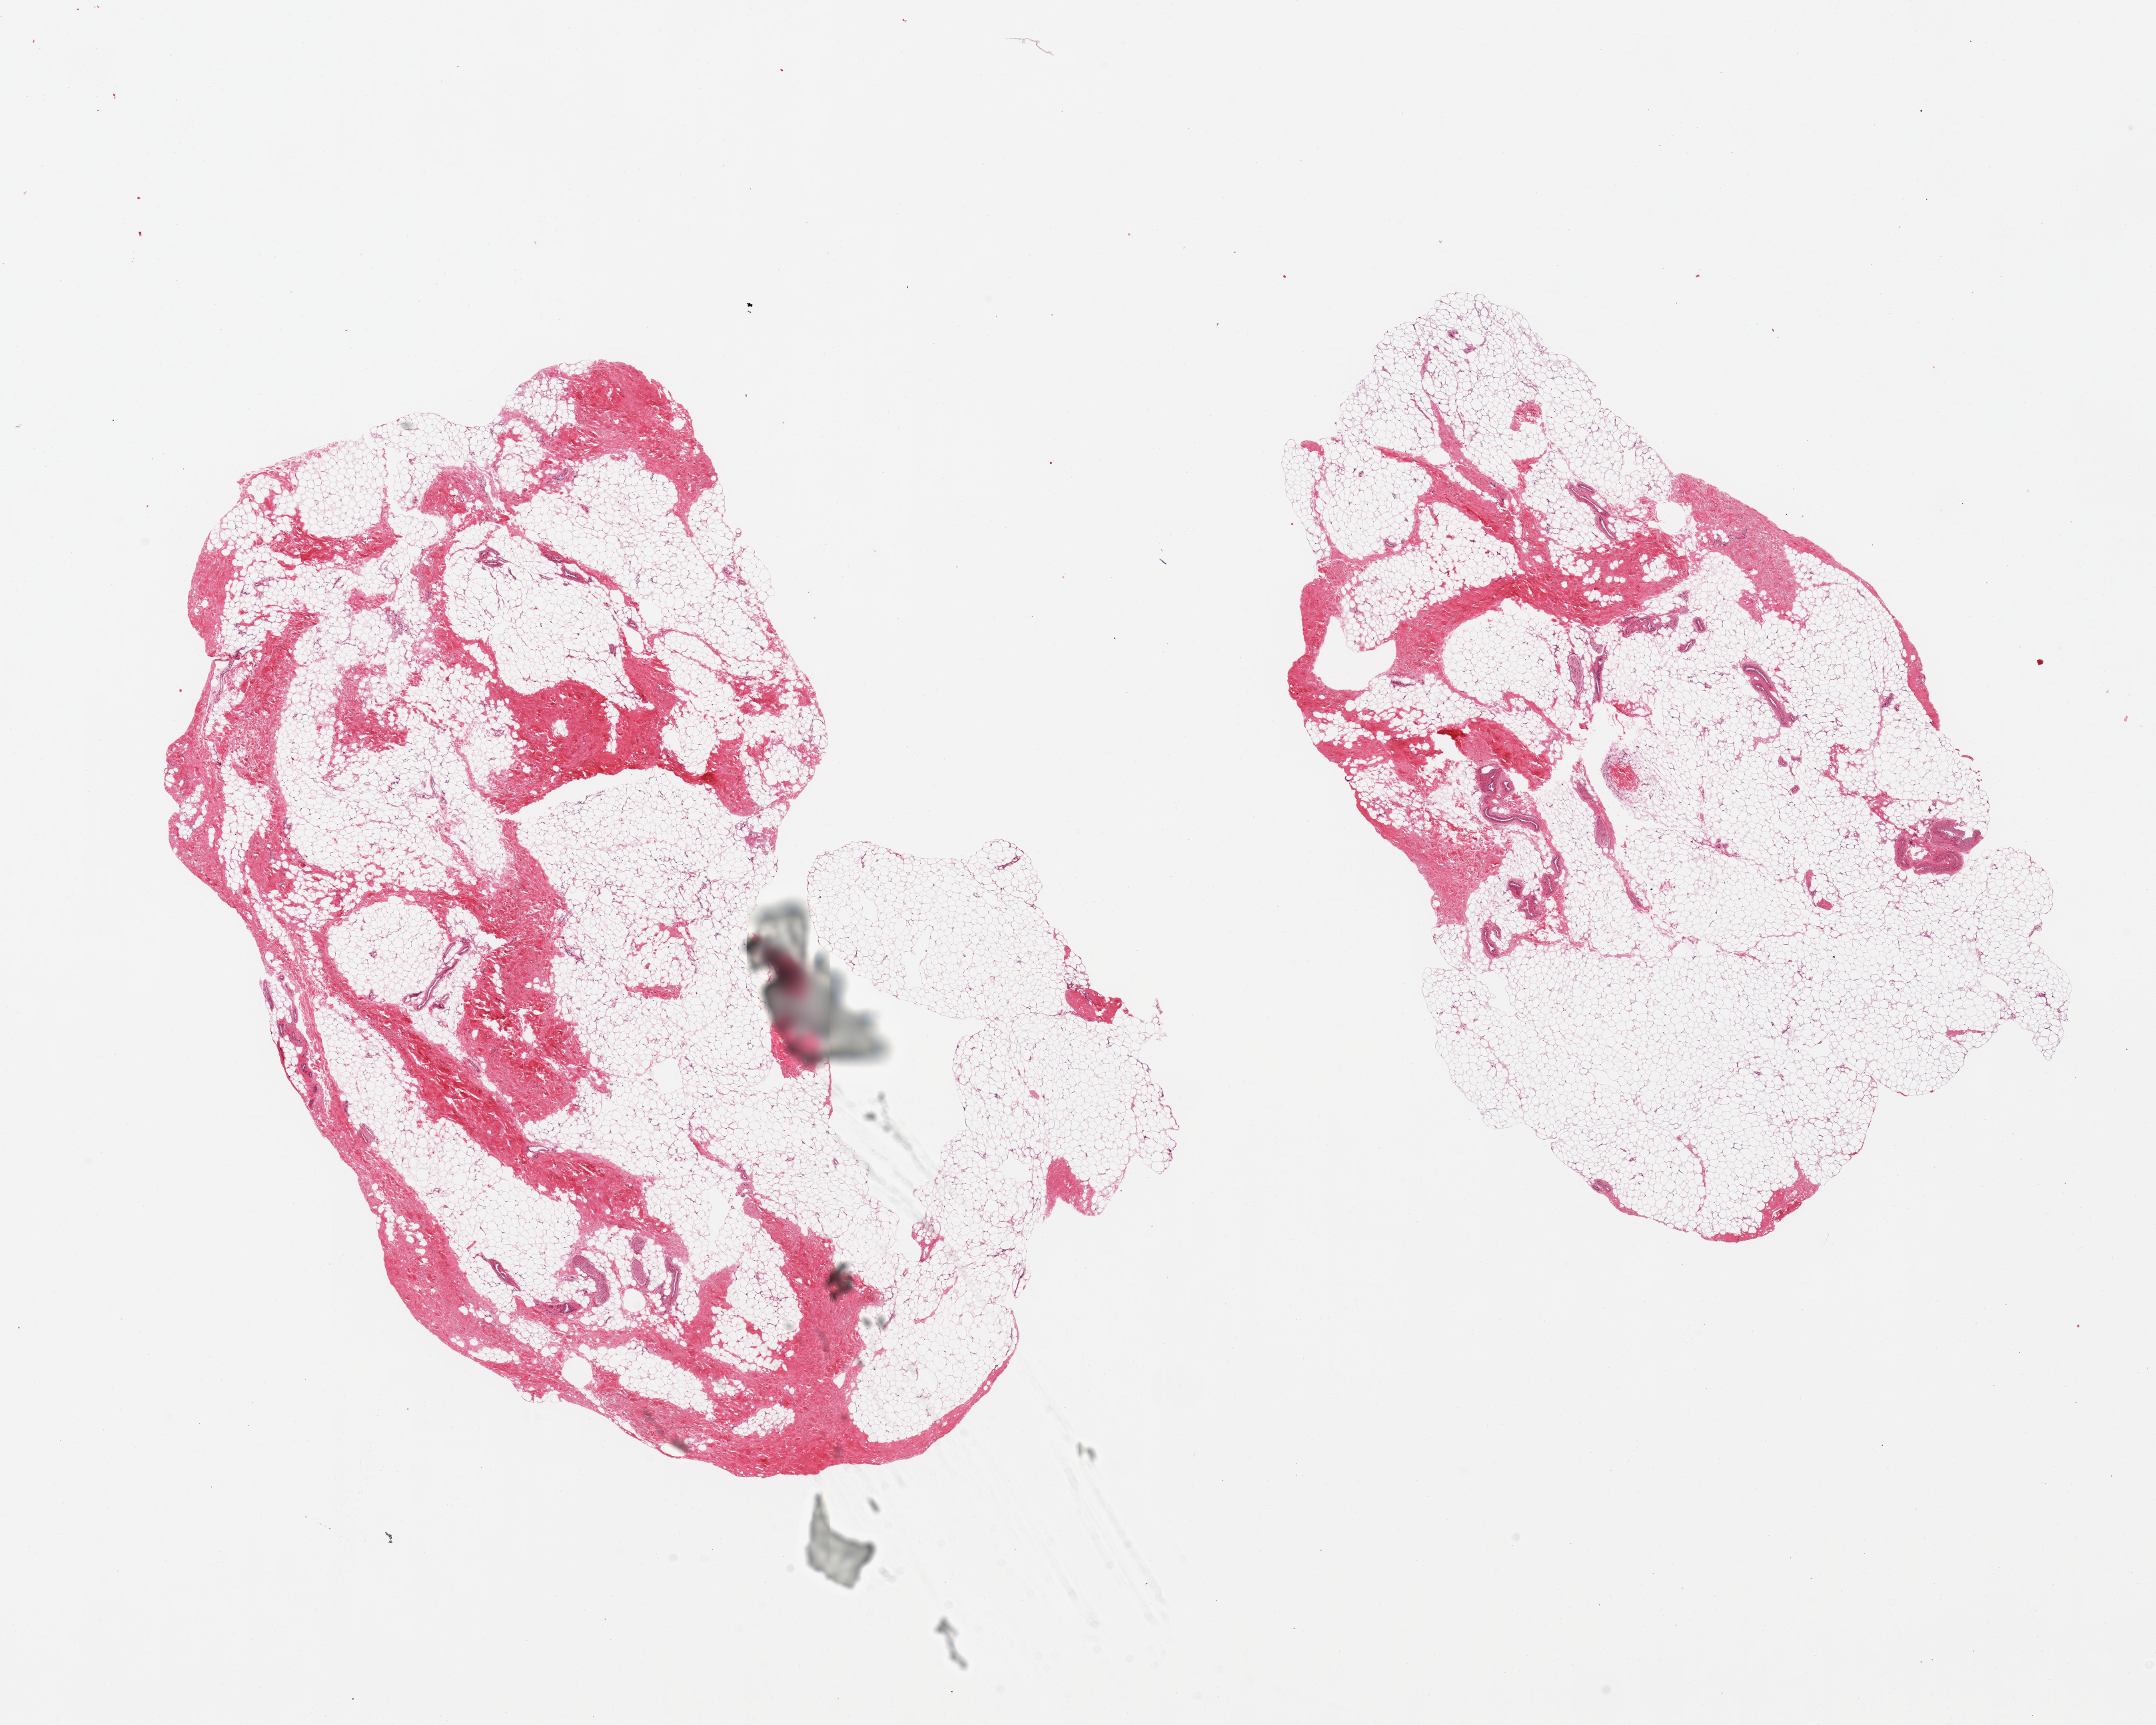
Hematoxylin and eosin (H&E) whole-slide image — shown as a low-resolution overview of the whole scanned area (about 25.6 x 20.5 mm). PAXgene-fixed paraffin-embedded (PFPE) section. Section of breast (target tissue). Tissue donor sample. Donor sex: male.
Pathologist's review note for this sample: 2 pieces, fibroadipose elements only.